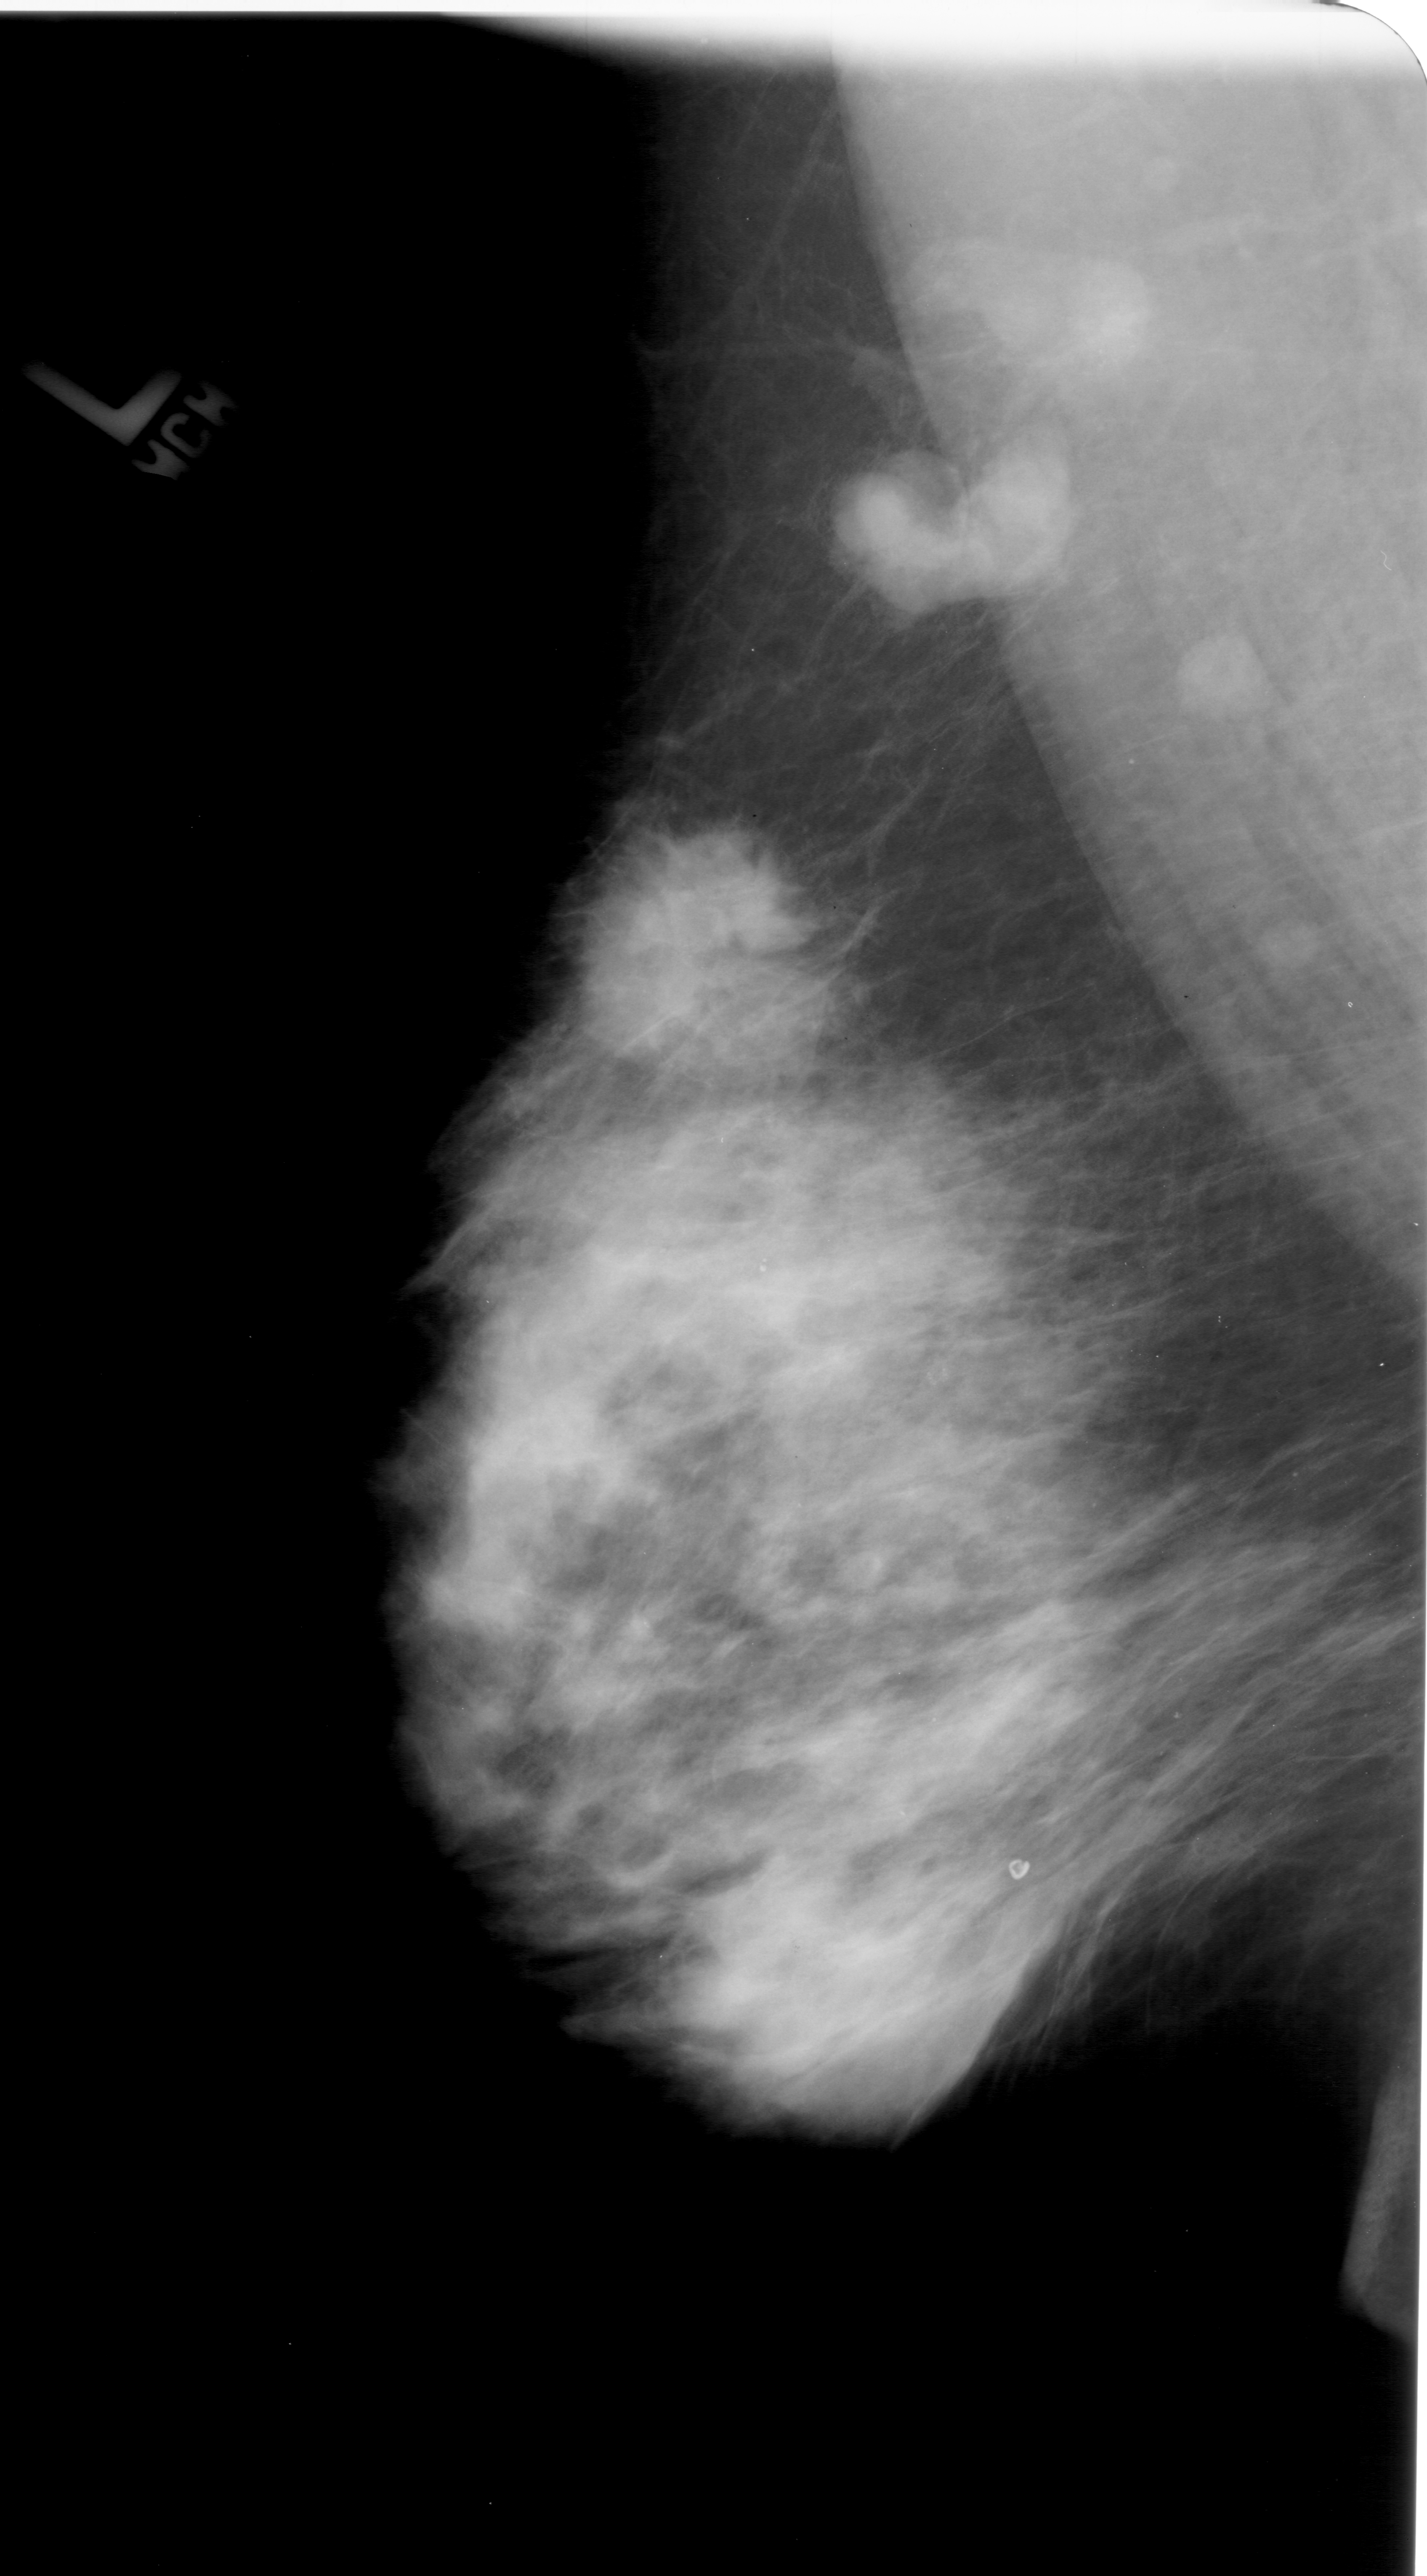
Digitized screen-film mammogram; left breast; mediolateral oblique (MLO) view; BI-RADS breast density category 4 (scale 1–4); 1427 × 2576 image matrix.
Marked abnormalities (boxes around the expert regions of interest):
- mass, shape irregular, margins spiculated; BI-RADS assessment category 5; subtlety rating 5 on a 1 (subtle) to 5 (obvious) scale; pathology (as recorded): malignant: box from (x=561, y=842) to (x=798, y=1062) px